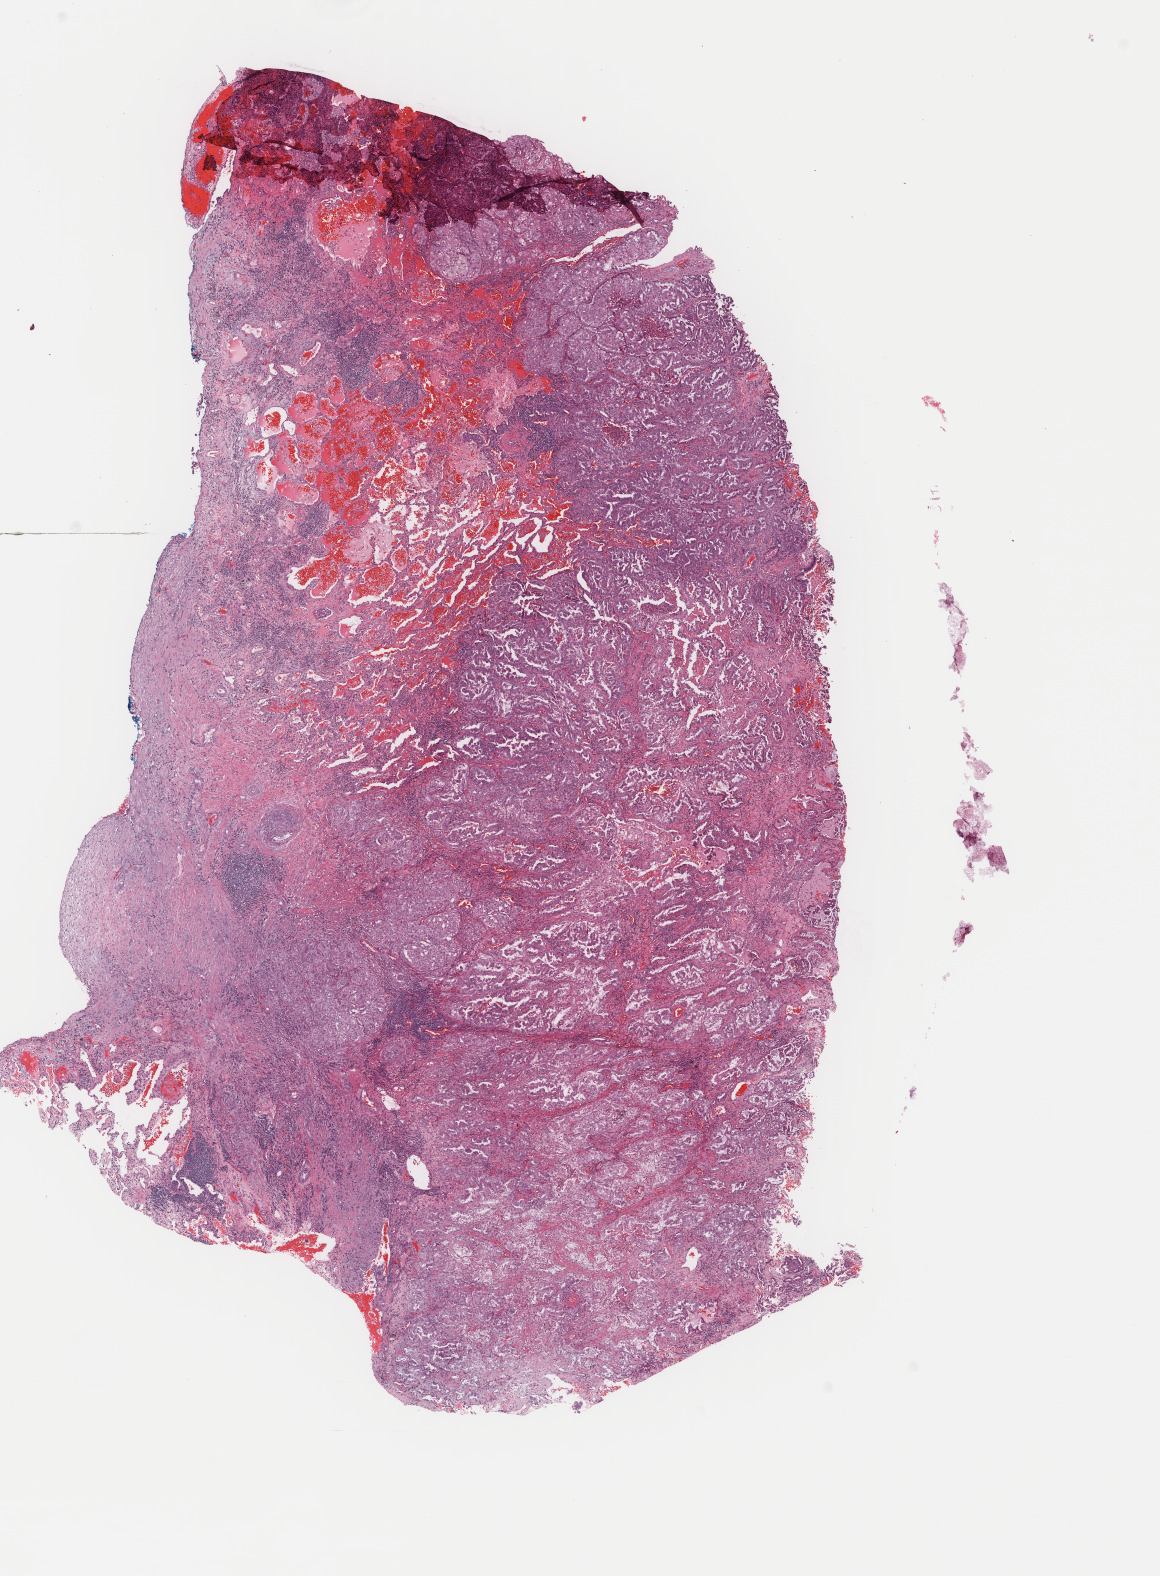
Digitized H&E tissue section (whole slide), a low-resolution overview of the entire scanned area, about 9.2 x 12.5 mm (slide scanned at 40x); frozen section from the bottom of the tissue portion; sample: primary tumour, lung. Female patient; age at initial diagnosis 60 years. Pathologist review of this section (percent, as recorded): tumour cells 70%, tumour nuclei 70%, normal cells 2%, stromal cells 27%, necrosis 1%. Infiltration values recorded for this section: lymphocyte infiltration 5%, monocyte infiltration 2%, neutrophil infiltration 2%.
AJCC pathologic stage: IB (6th edition). Histologic diagnosis: Adenocarcinoma, NOS (upper lobe, lung). Laterality: right.